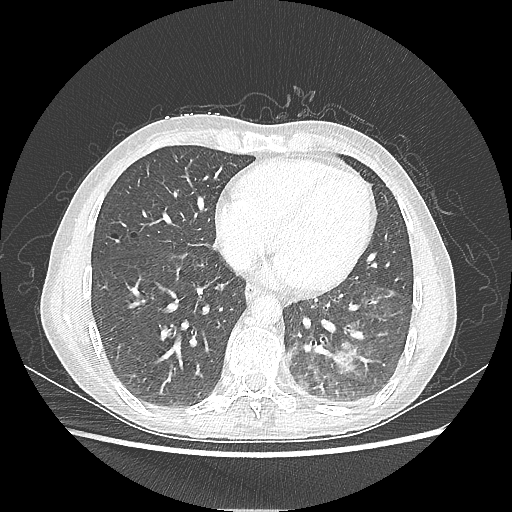
Chest CT, one axial slice; slice 81 of 220 in the series (ordered by position); reconstruction kernel LUNG; 80 kVp; lung window (W 1500 / L -600 HU); 512 × 512 image matrix, field of view 360 × 360 mm. Female patient, age 53 years. Case-level facts recorded for this patient, not image findings: clinical TNM (as recorded): T3 N0 M0.
Annotated regions visible in this slice (bounding box drawn by a radiologist):
- lung tumour (recorded histology: adenocarcinoma): box from (x=312, y=339) to (x=358, y=375) px